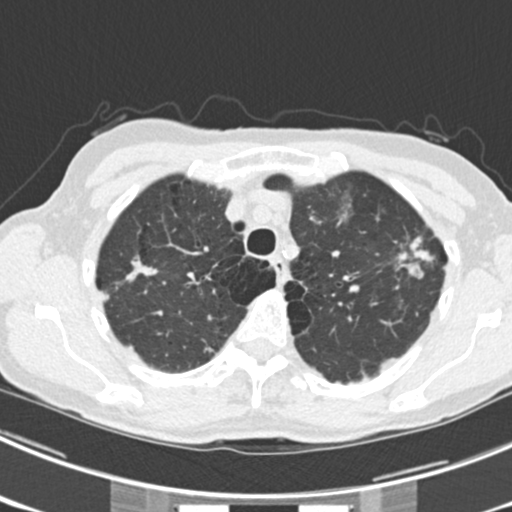
Low-dose screening chest CT, one axial slice. Slice 176 of 225 in the series (ordered by position). Reconstruction kernel B30f. 120 kVp. Lung window (W 1500 / L -600 HU). 2 mm slice thickness. 512 × 512 image matrix, field of view 302 × 302 mm.
Outlined on this slice (outlined manually by an expert reader):
- lesion 1 (tumor, upper lobe of left lung): bounding box <394,237,434,279> (left, top, right, bottom; pixels)
- lesion 5 (tumor, upper lobe of right lung): <121,257,158,286>